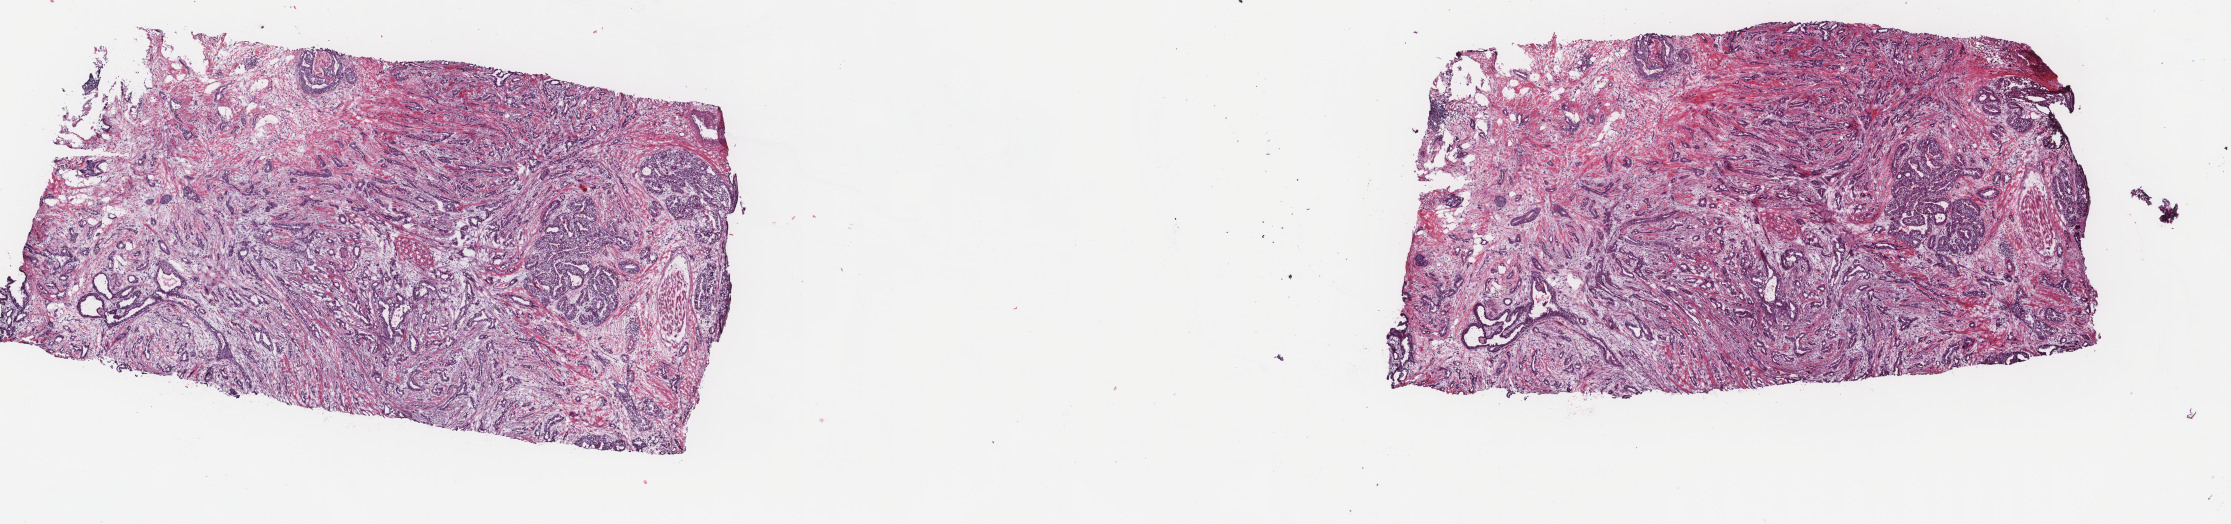
Digitized H&E-stained tissue section (whole slide) — shown as a low-resolution overview of the whole scanned area (about 17.7 x 4.2 mm, slide scanned at 40x), frozen section from the top of the tissue portion, sample: primary tumour, breast. Patient: female, age at initial diagnosis 52 years. Composition of this section per pathologist review: tumour cells 60%, tumour nuclei 70%, normal cells 0%, stromal cells 40%, necrosis 0%. Inflammatory infiltration, as recorded: lymphocyte infiltration 0%, monocyte infiltration 0%, neutrophil infiltration 0%.
• lymph nodes positive (case pathology): 1 of 12 examined
• AJCC pathologic stage: IIIA
• histologic diagnosis: Lobular carcinoma, NOS